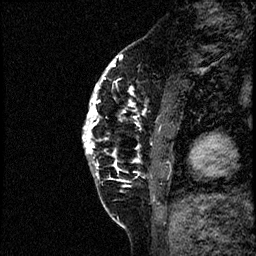
Breast MRI (dynamic contrast-enhanced), one sagittal slice. Slice 15 of 60 in the series (ordered by position). Dynamic contrast-enhanced study with each time point stored as its own series, time point 2 of 4 at this slice position (early post-contrast, ordered by acquisition time). 1.5 T. TE 4.2 ms, TR 17.6 ms. 2 mm slice thickness. 256 × 256 image matrix, field of view 200 × 200 mm. Patient: female, 40 years. Case-level facts recorded for this patient, not image findings: setting: breast cancer imaged before/during neoadjuvant chemotherapy; receptor status: HER2-positive.
Structures marked on this image (semi-automatically segmented with operator editing):
- analysis volume of interest (the breast-tissue region the enhancement analysis was run in; not a lesion): bounding box <83,56,197,205> (left, top, right, bottom; pixels)
- tumour enhancement mask (voxels above the 100 % enhancement threshold inside the analysis volume of interest): <84,56,140,182>